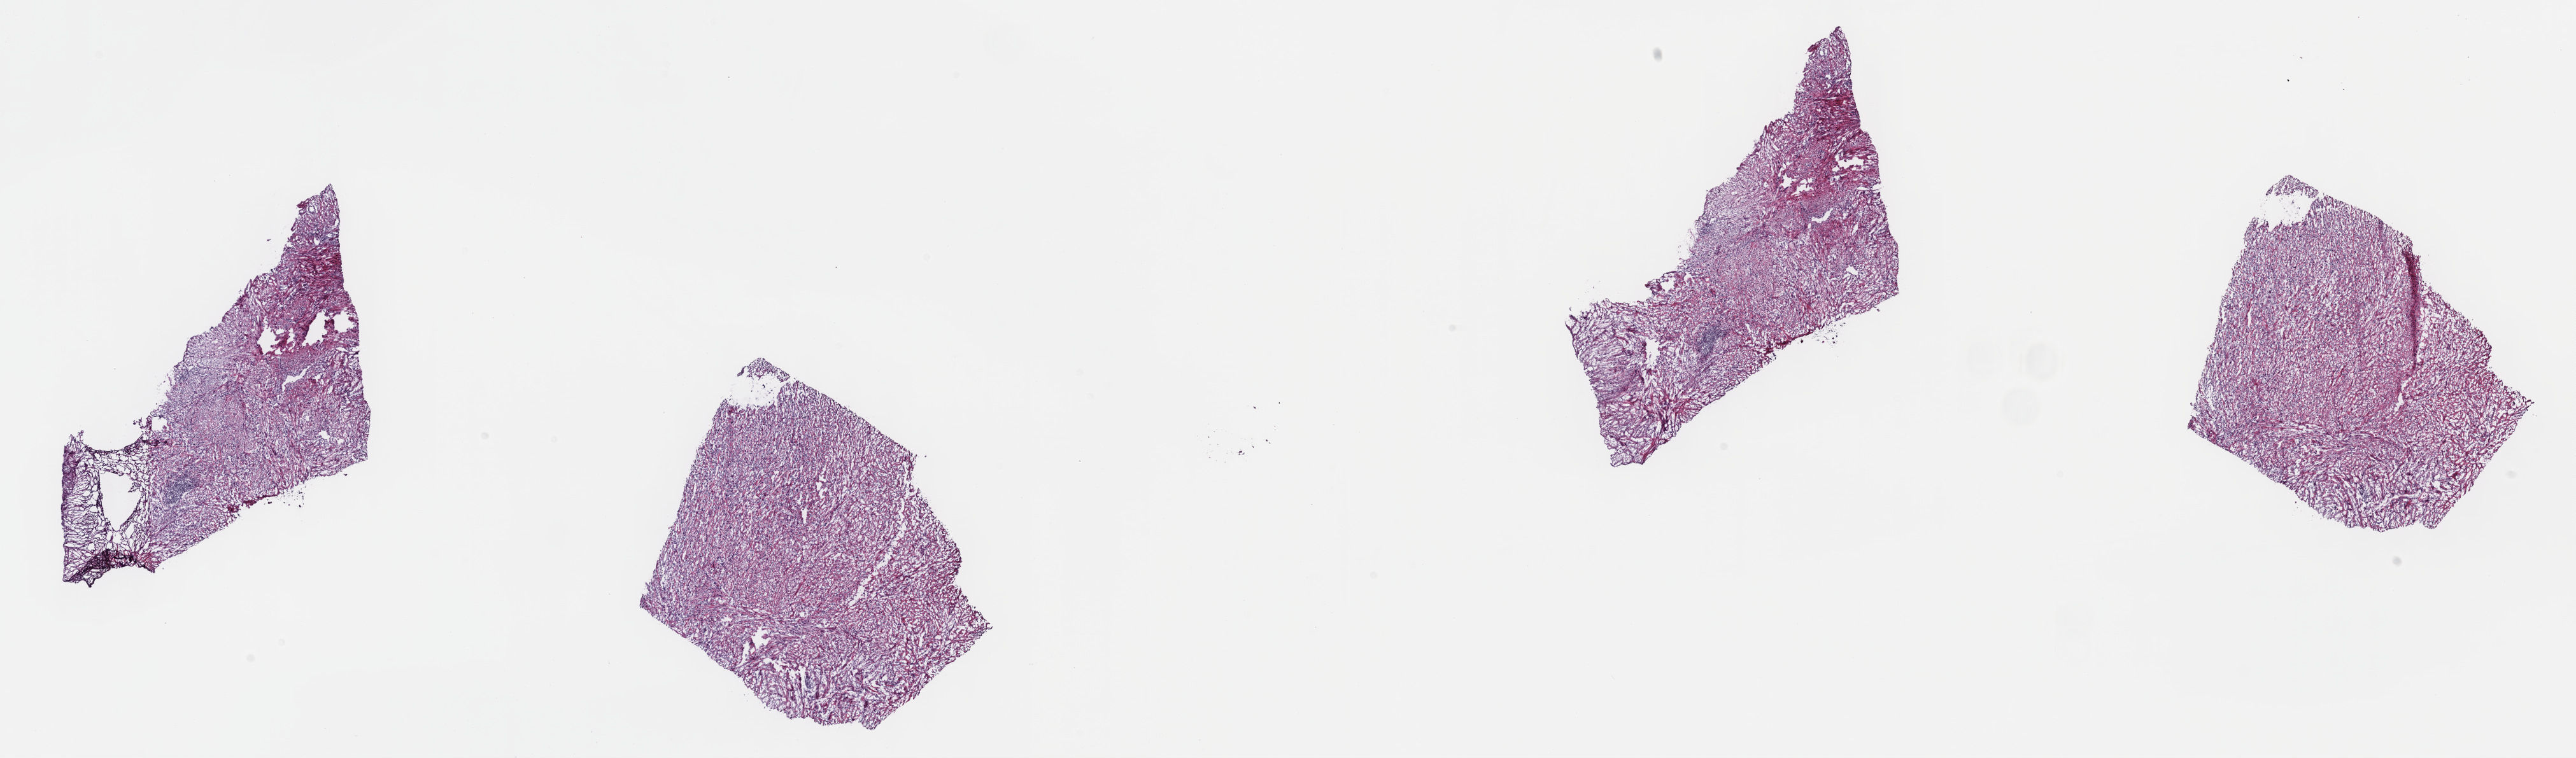
Whole-slide histology image, Hematoxylin and eosin (H&E) stained, a low-resolution overview of the entire scanned area, about 32.7 x 9.6 mm; frozen section; primary tumour sample from the retroperitoneum and peritoneum. Male, age 60 years at initial diagnosis. Pathologist review of this section (percent, as recorded): tumour cells 100%, tumour nuclei 80%, normal cells 0%, stromal cells 0%, necrosis 0%. Inflammatory infiltration, as recorded: lymphocyte infiltration 1%, monocyte infiltration 0%, neutrophil infiltration 0%.
Pathologic diagnosis: Myxoid leiomyosarcoma (retroperitoneum).